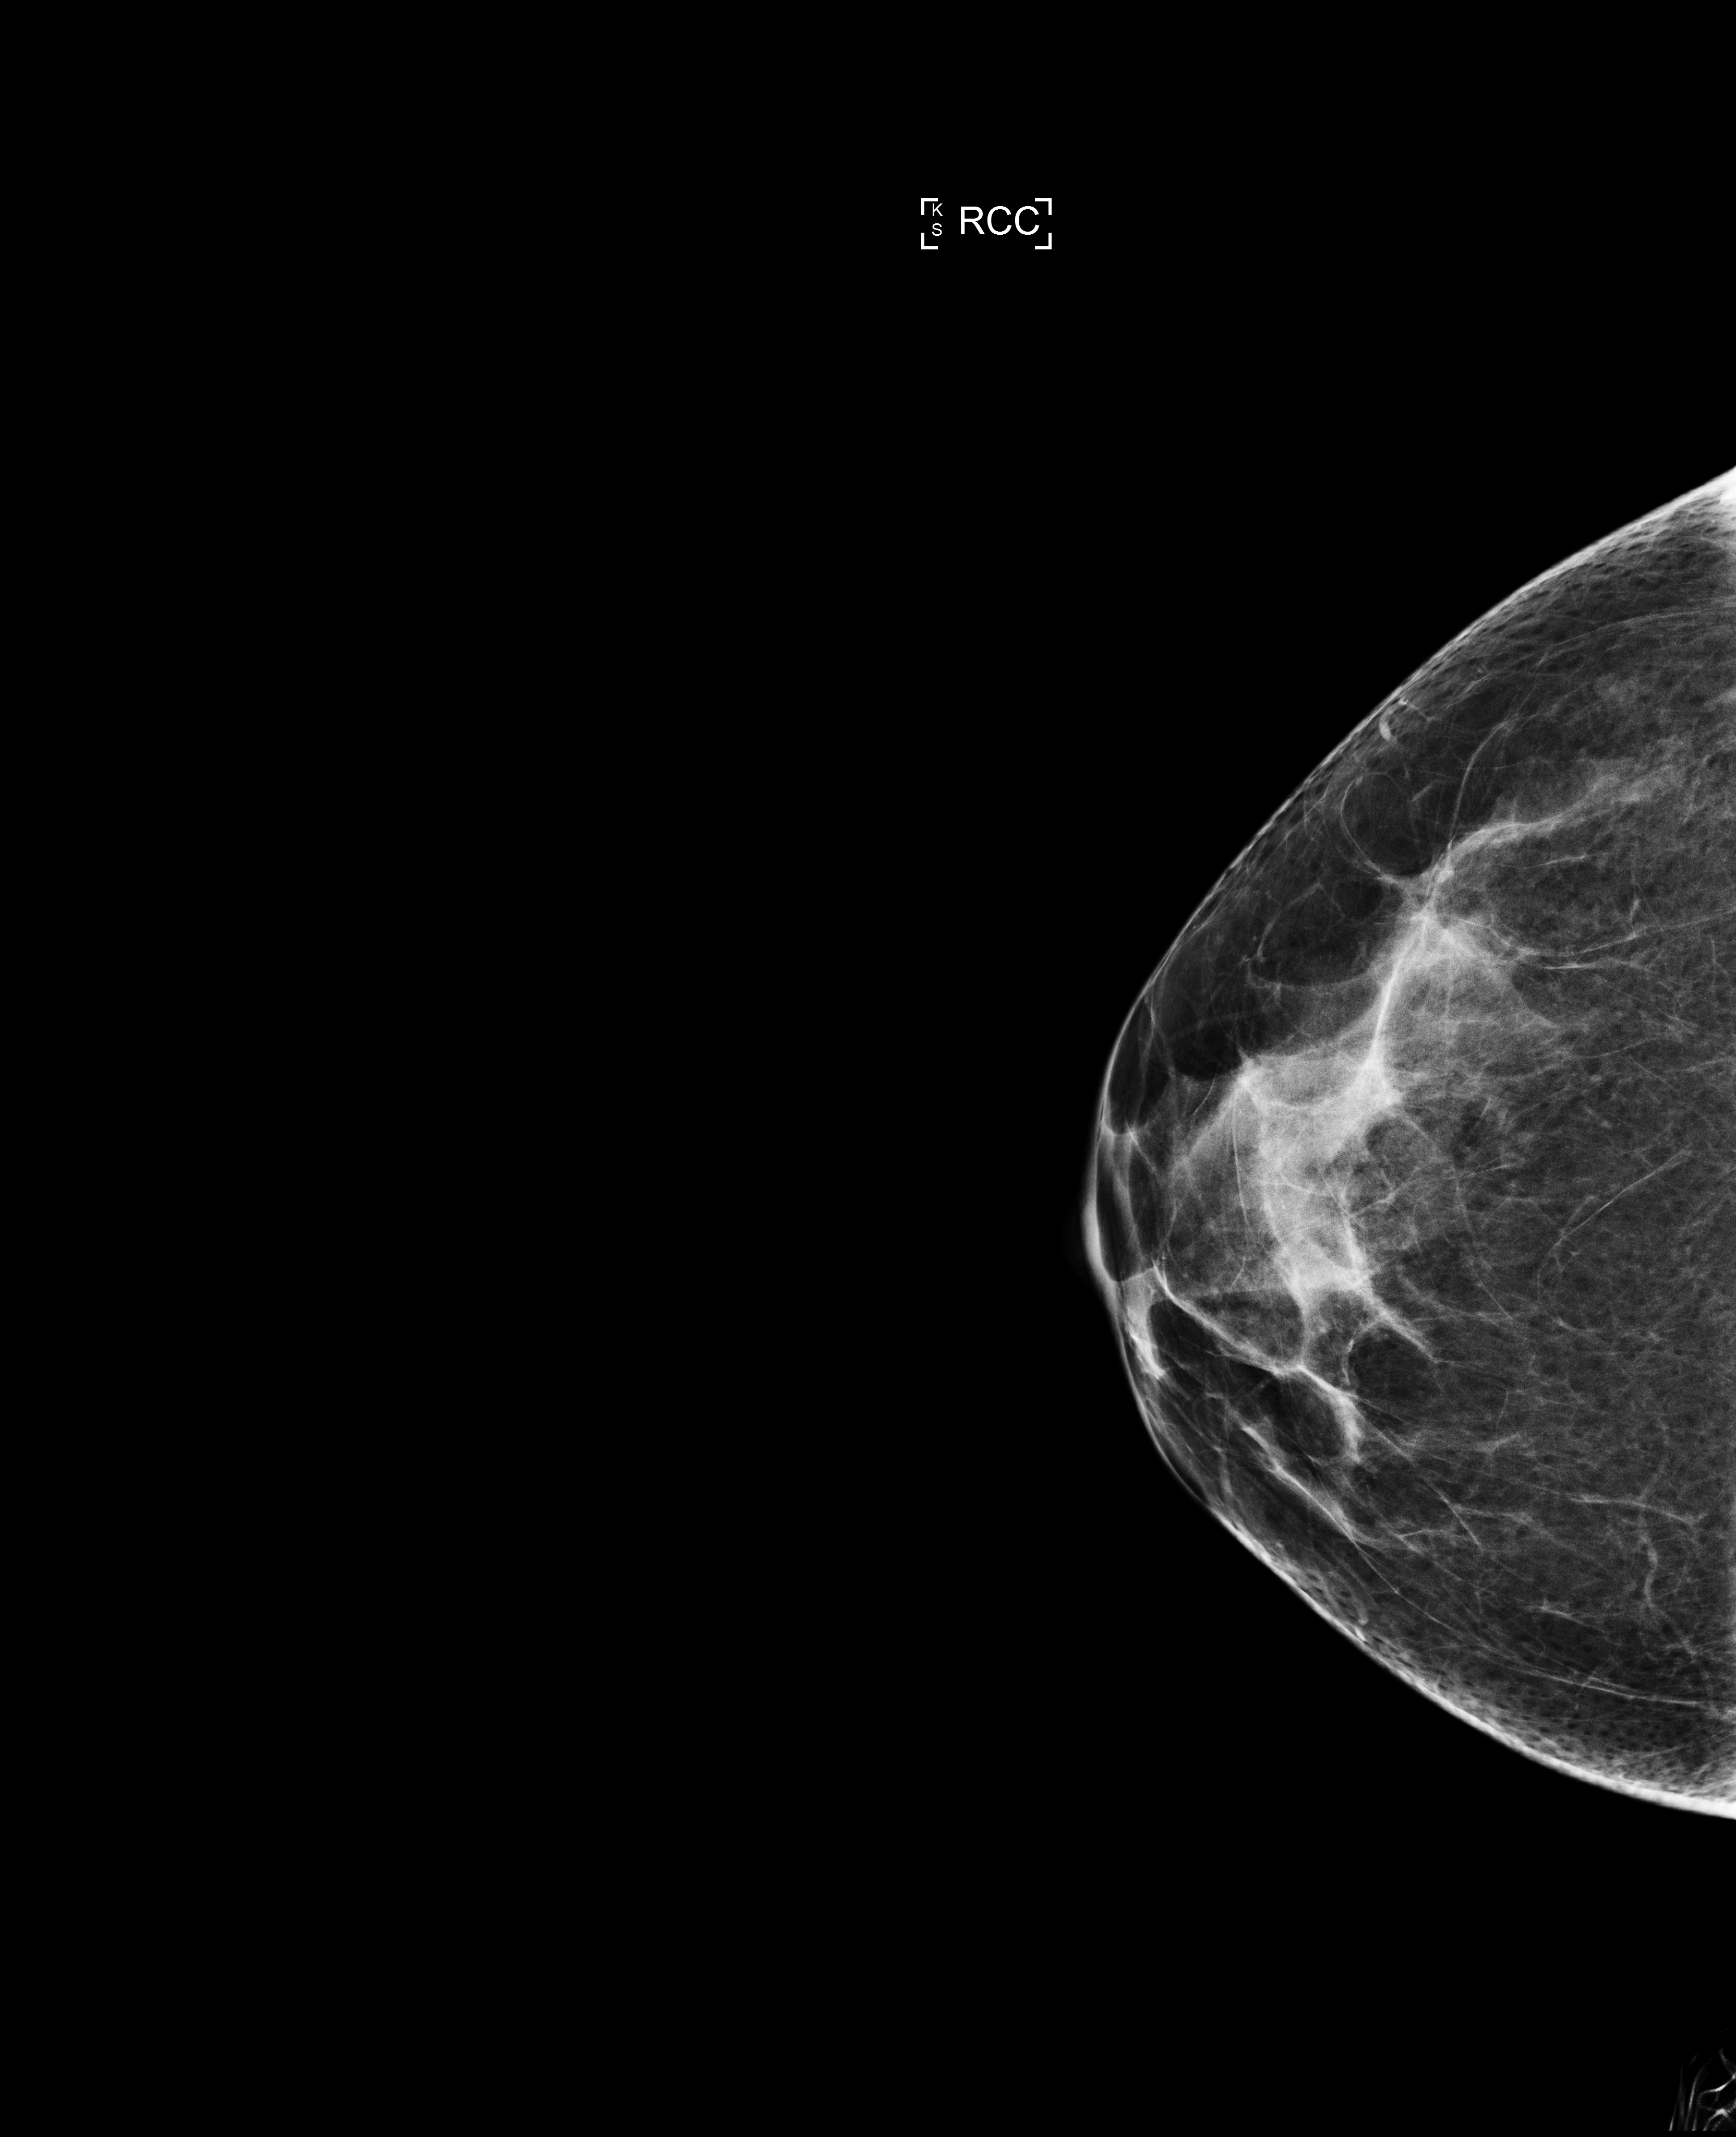
Digital mammogram (FFDM), right breast, CC view, diagnostic work-up study, compressed breast thickness 57 mm. Patient: female, 49 years.
Breast density at the screening exam (both breasts): heterogeneously dense (BI-RADS density category c). Final BI-RADS category for the screening round (tomosynthesis exam, both breasts): category 2. Recall: recalled for additional imaging after this screen.